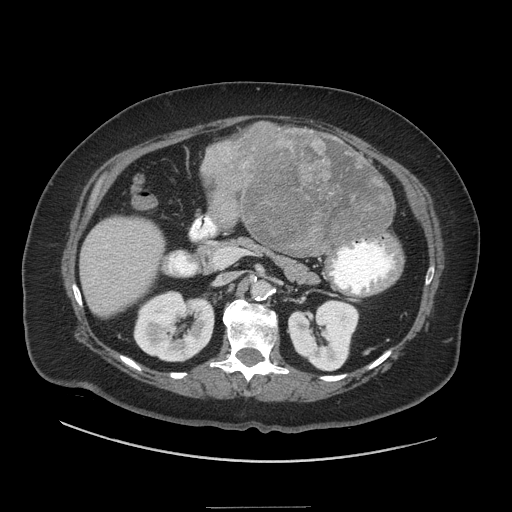
Contrast-enhanced abdominal CT (liver protocol), one axial slice. Position 11 of 81 along the scan axis. Soft-tissue window (W 400 / L 40 HU). 512 × 512 image matrix, field of view 440 × 440 mm. Case-level facts recorded for this patient, not image findings: diagnosis: hepatocellular carcinoma (patient treated with transarterial chemoembolisation; whether this scan precedes or follows treatment is not stated here); TNM stage (as recorded): Stage-II; Child-Pugh class: A; tumour differentiation: moderately differentiated; tumour size: 1.7 cm.
Outlined on this slice (semi-automatically segmented with operator editing):
- liver parenchyma outside the tumour (the mass and vessels are separate outlines, so this box may not span the whole liver): box from (x=80, y=156) to (x=394, y=316) px
- mass: (x=199, y=121)–(x=395, y=255)
- liver vessels: (x=102, y=233)–(x=137, y=269)